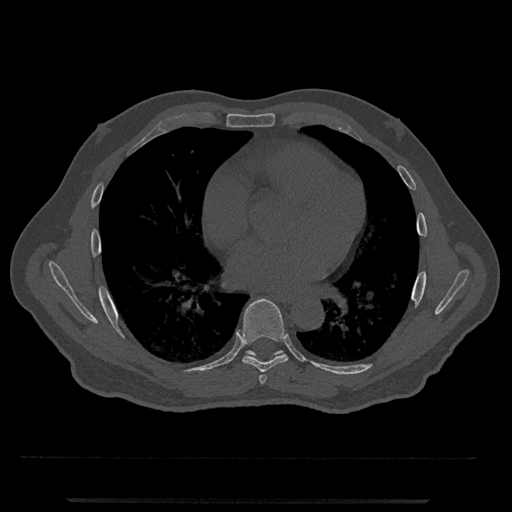
CT including the spine, one axial slice. Position 673 of 797 along the scan axis. 120 kVp. Bone window (W 1800 / L 400 HU). 0.5 mm slice thickness. 512 × 512 image matrix, field of view 419 × 419 mm. Patient: male, 63 years. Case-level facts recorded for this patient, not image findings: primary cancer: prostate.
Structures marked on this image (semi-automatically segmented with operator editing):
- T6 vertebra: box from (x=259, y=375) to (x=267, y=384) px
- T7 vertebra: (x=236, y=298)–(x=289, y=372)
- T8 vertebra: (x=246, y=350)–(x=284, y=356)